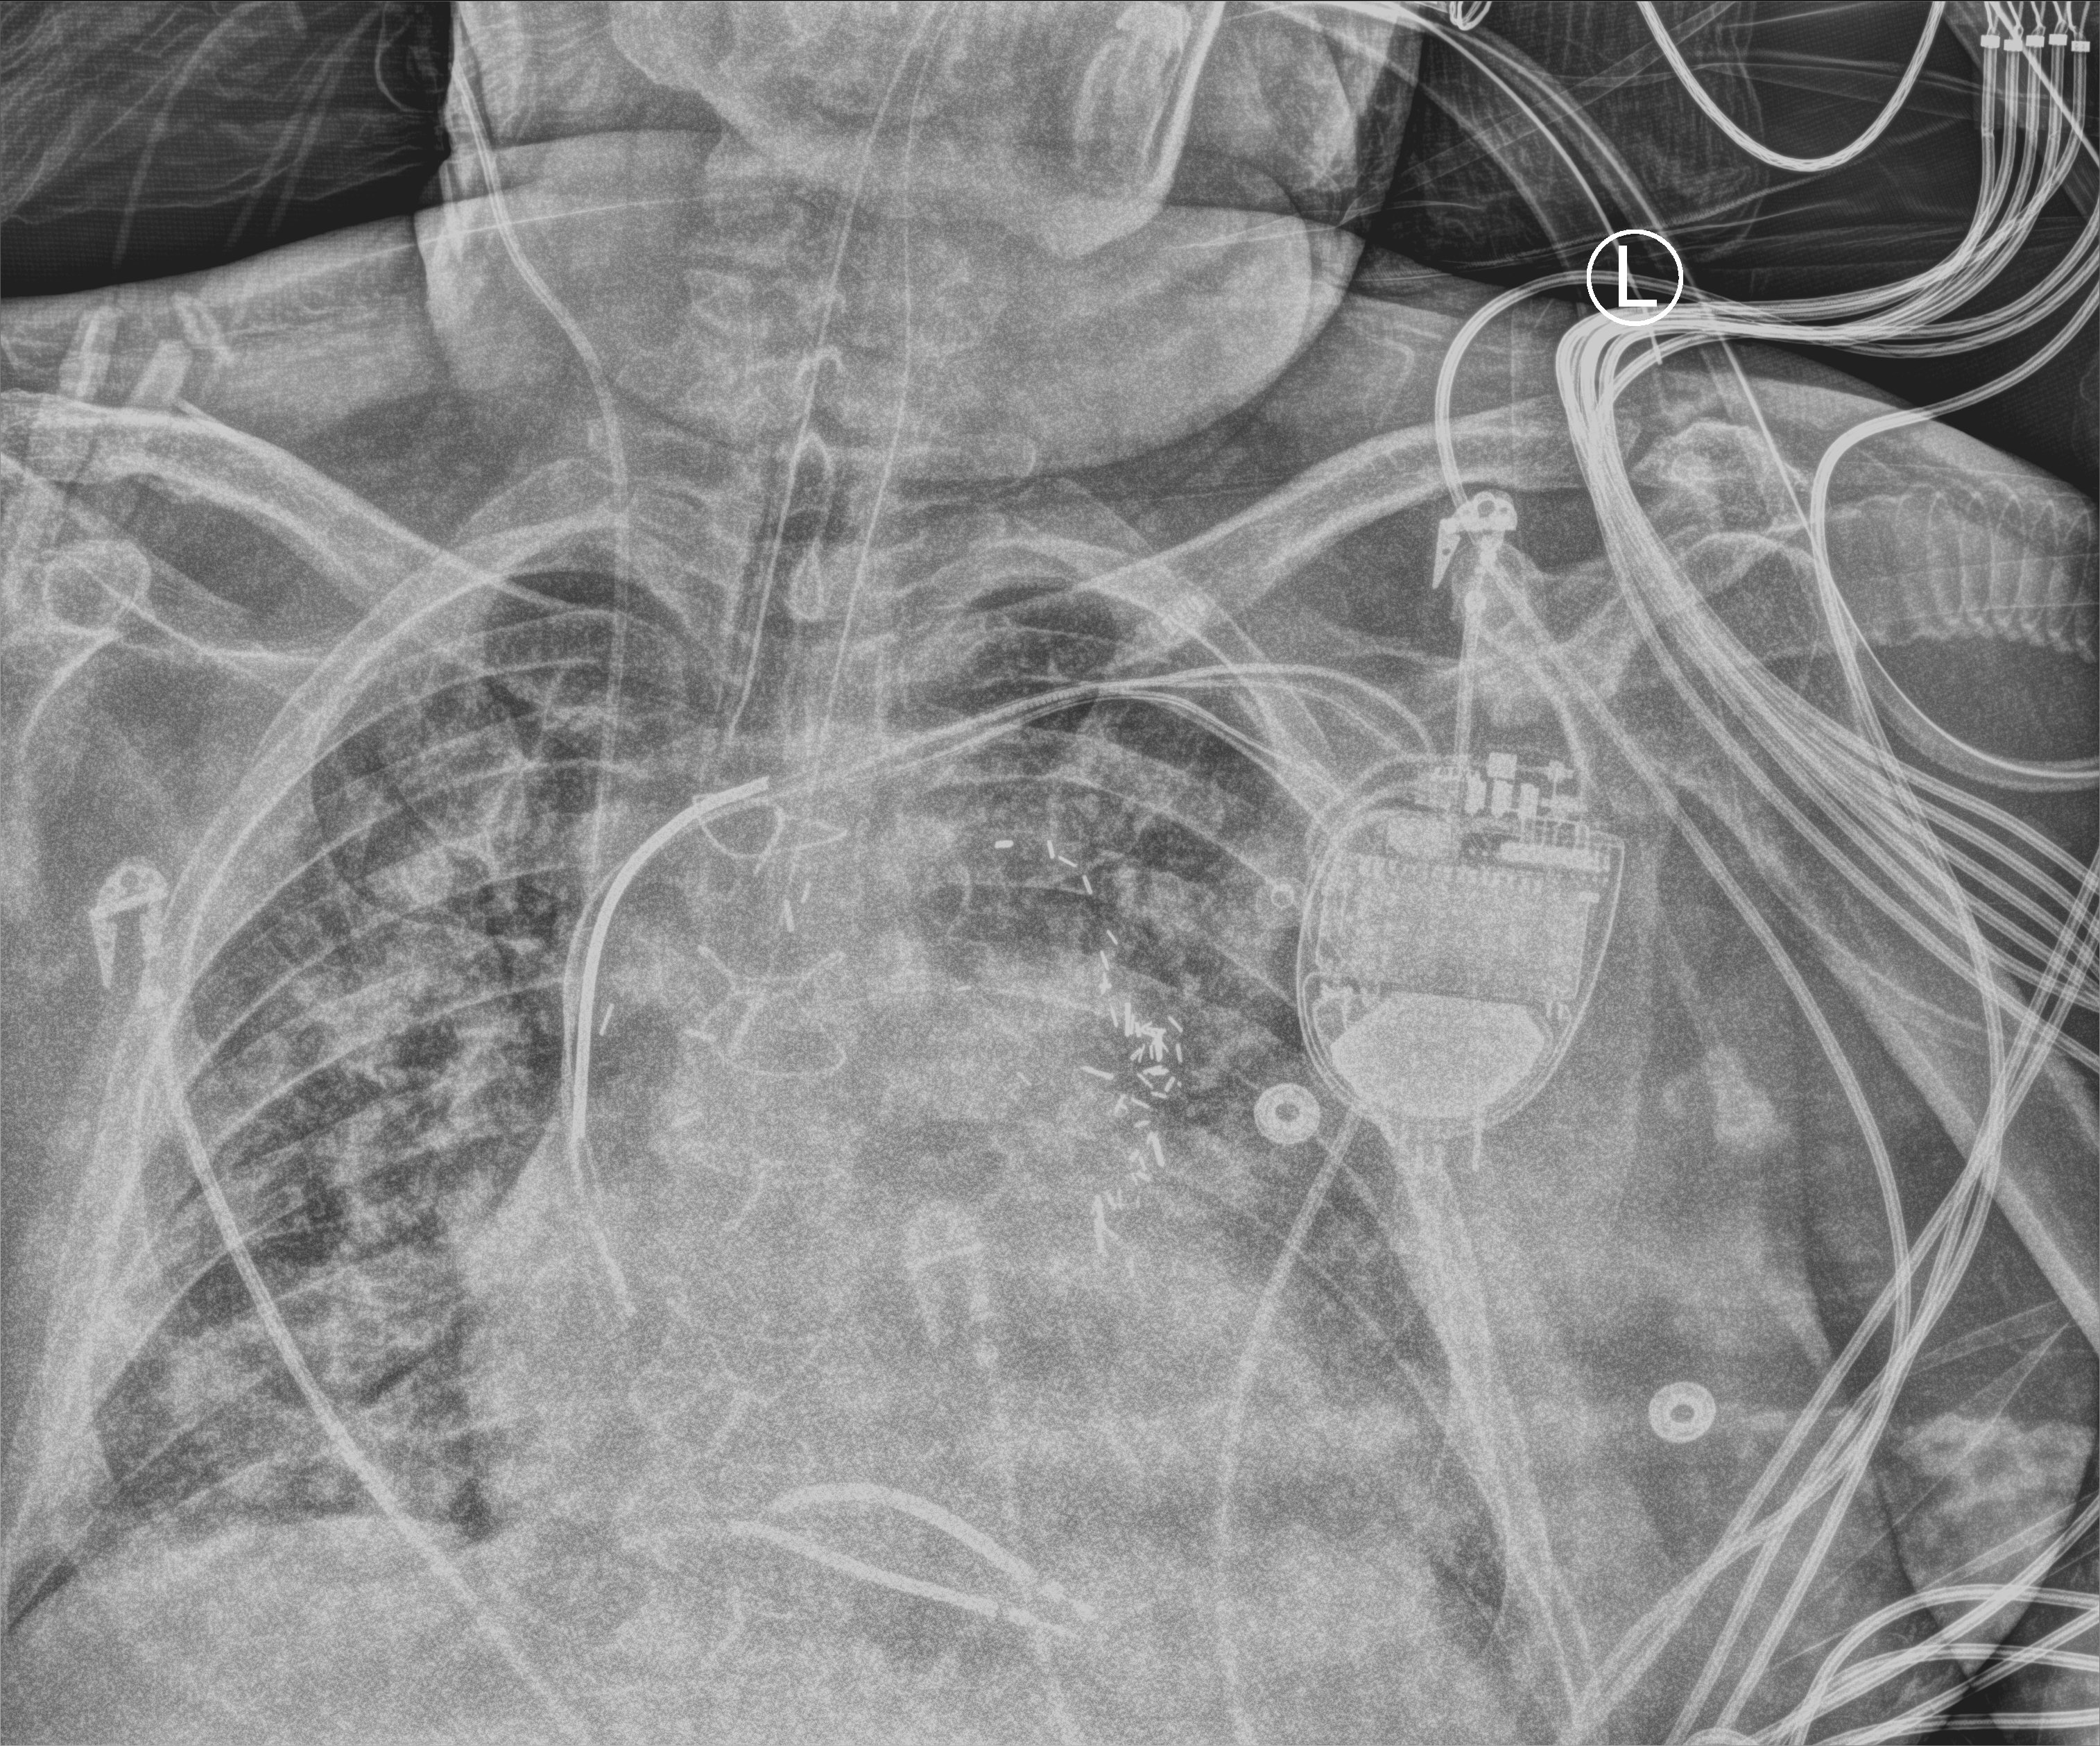
Chest X-ray (portable), anteroposterior (AP) projection. Male patient hospitalised with COVID-19, age 60–74 years.
Hospital-stay facts (about this admission, not read from this image; timing relative to this image not recorded): mechanically ventilated during this hospital stay: yes.